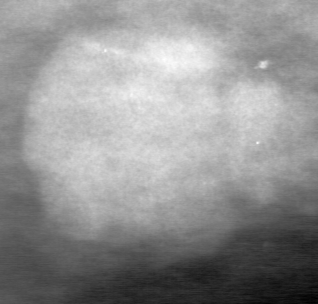
Crop from a digitized film mammogram around one marked abnormality, left breast, CC view.
Marked abnormality: mass, shape lobulated, margins microlobulated; BI-RADS assessment category 3; pathology result (as recorded, not read from the image): benign.